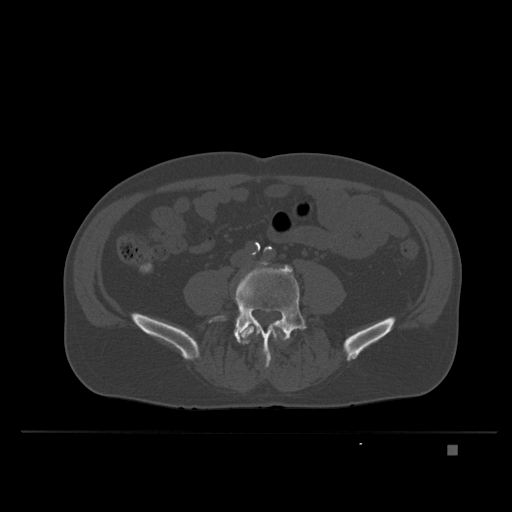
CT including the spine, one axial slice; slice 62 of 435 in the series (ordered by position); bone window (W 1800 / L 400 HU); 512 × 512 image matrix, field of view 434 × 434 mm. Male patient, age 73 years. Case-level facts recorded for this patient, not image findings: primary cancer: skin.
Outlined on this slice (semi-automatically segmented with operator editing):
- L4 vertebra: bounding box <239,318,285,366> (left, top, right, bottom; pixels)
- L5 vertebra: <215,265,308,345>